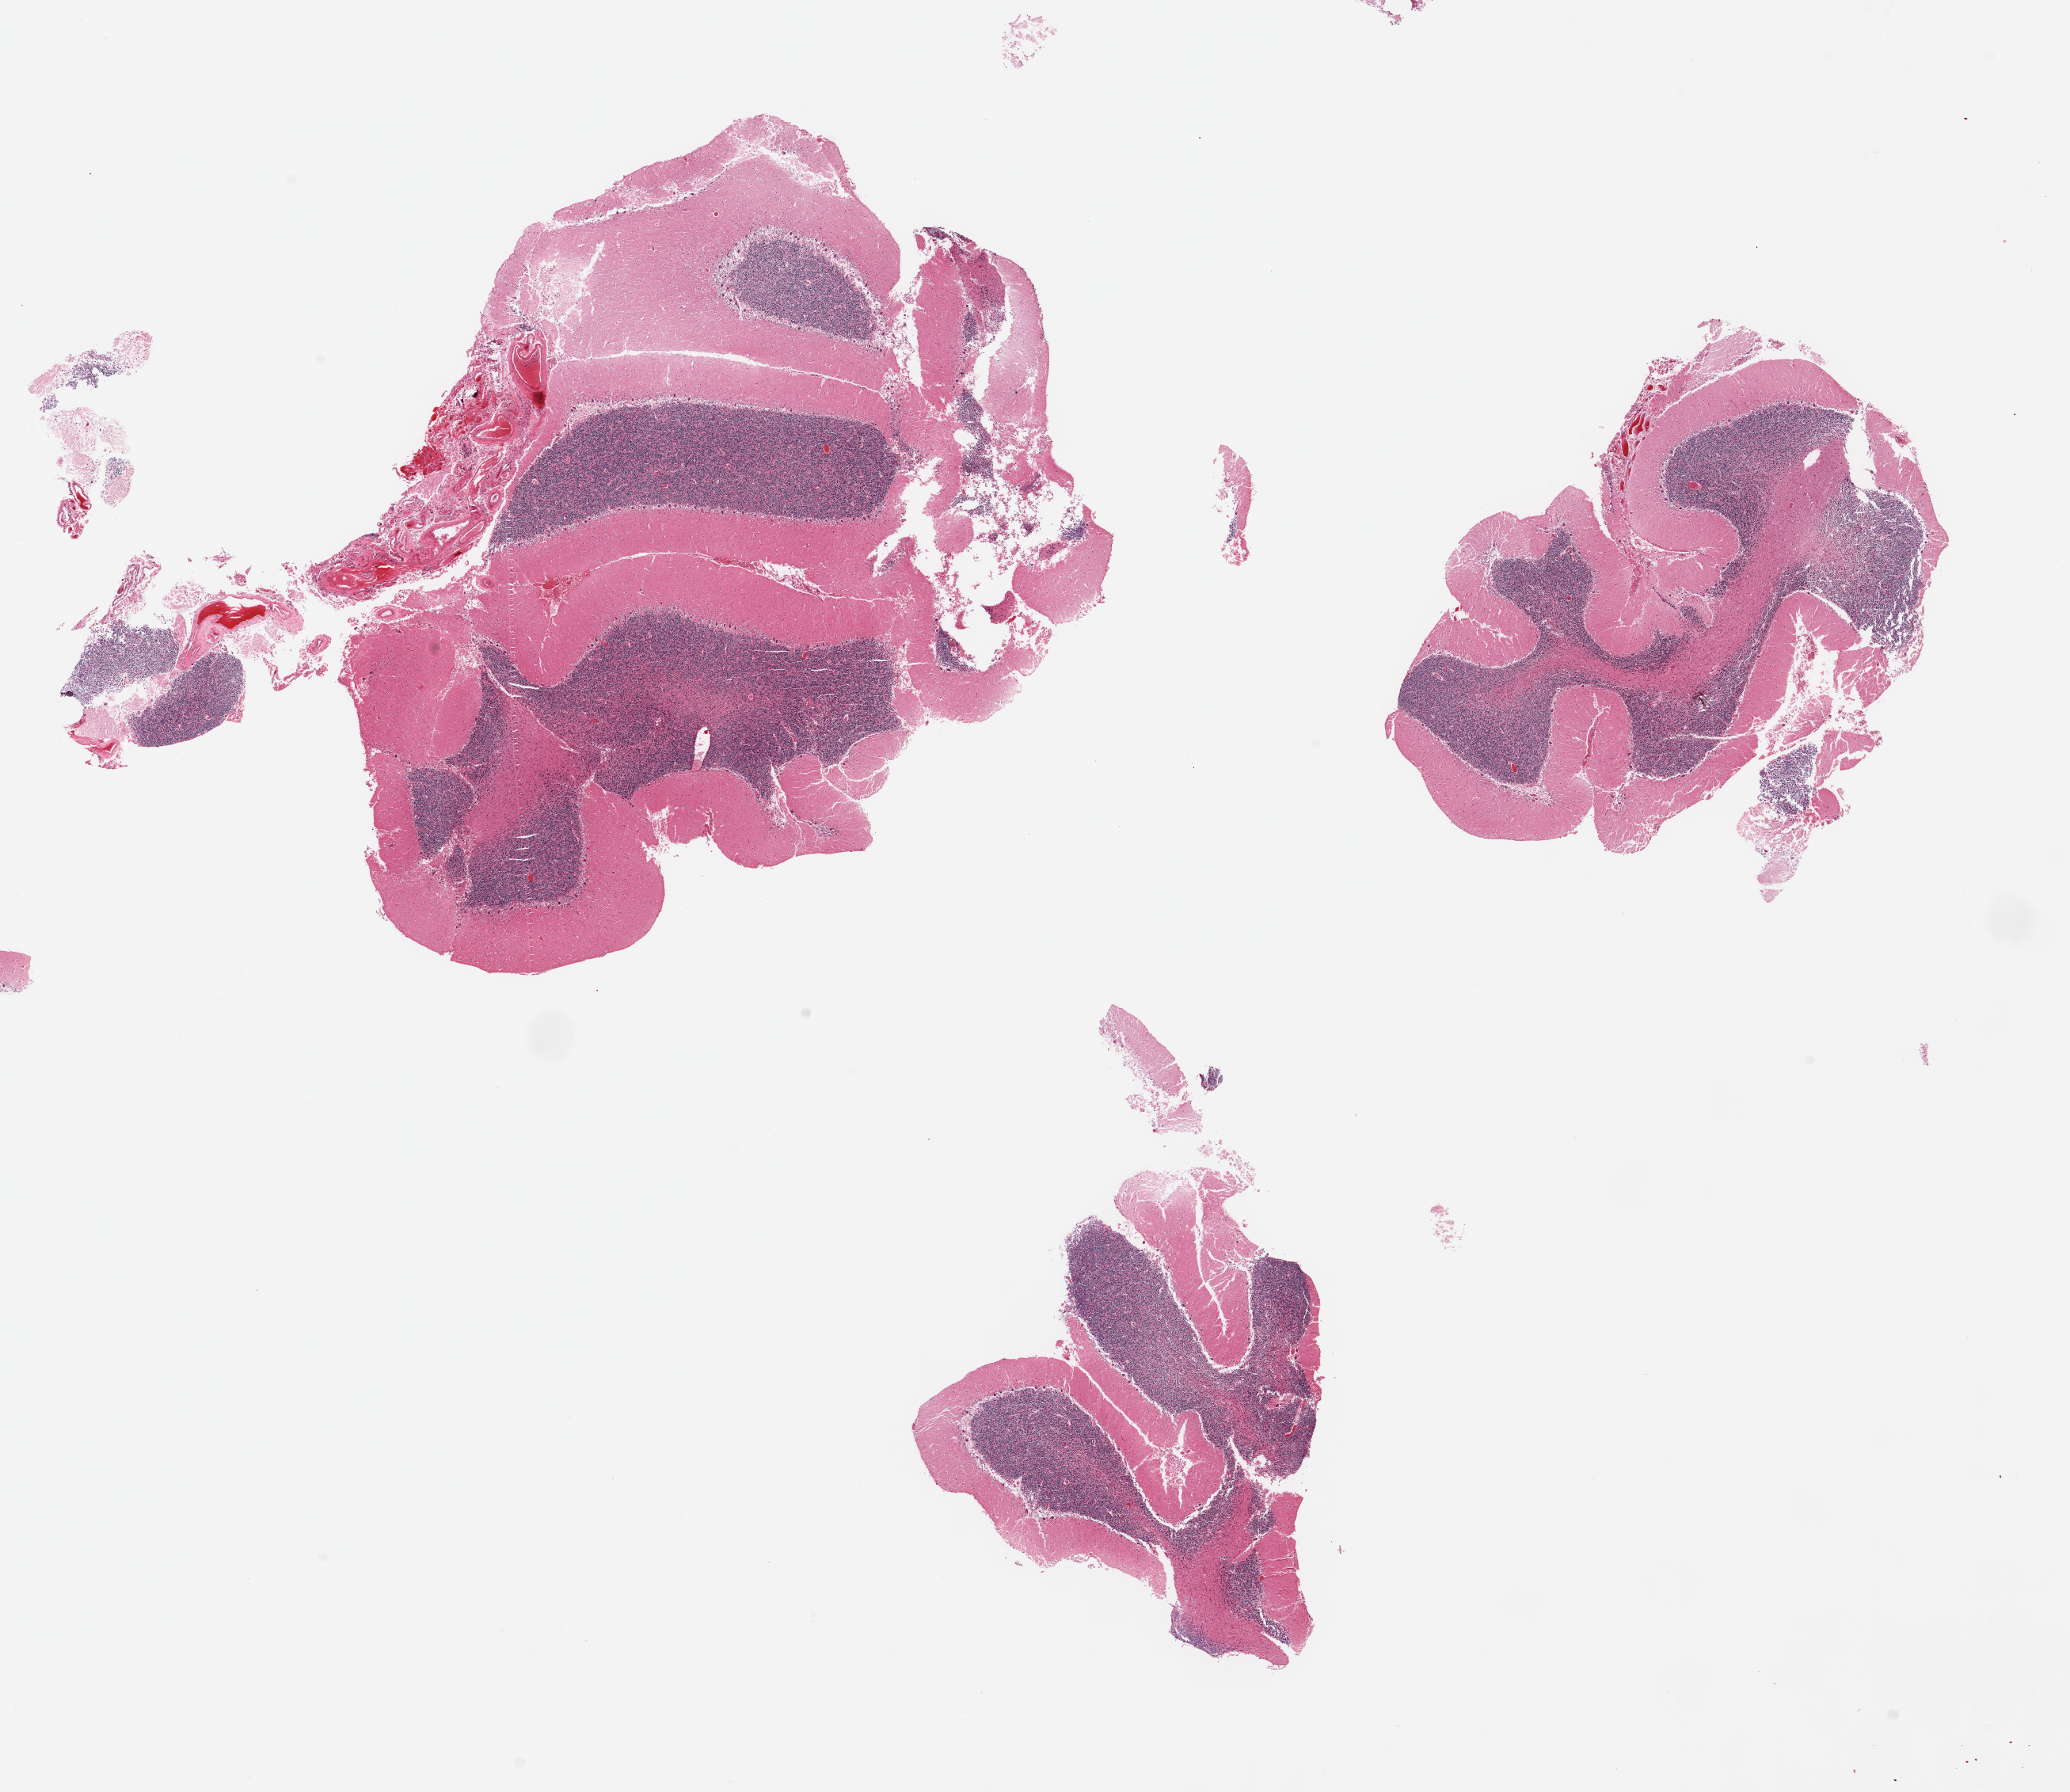
Whole-slide image, H&E stain, brightfield — whole scanned area (about 20.7 x 17.9 mm) shown as a low-resolution overview; PAXgene-fixed, paraffin-embedded tissue; section of cerebellum (target tissue); donor tissue sample. Donor: male.
• review note (as recorded): 3 pieces with fragmentation; cerebellum, not cortex, portion of attached meninges